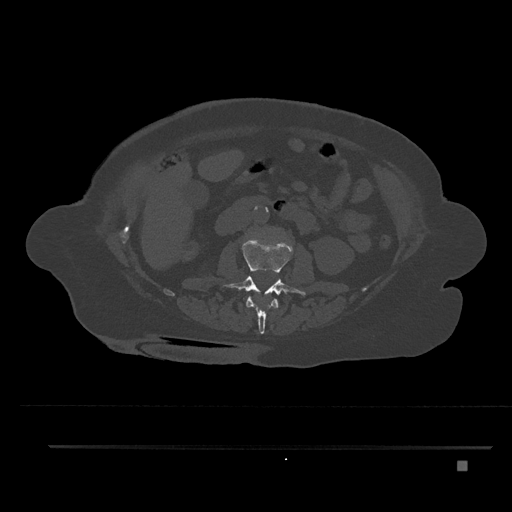
CT including the spine, one axial slice; reconstruction kernel Br40s/3; 120 kVp; bone window (W 1800 / L 400 HU); 512 × 512 image matrix. Patient: female, 76 years. From the clinical record (not read from this slice): primary cancer: lung; vertebrae with lytic lesions (as recorded): T11, L3.
Annotated regions visible in this slice (semi-automatic segmentation, software-assisted and operator-edited):
- L1 vertebra: box from (x=246, y=296) to (x=279, y=334) px
- L2 vertebra: (x=222, y=237)–(x=306, y=302)